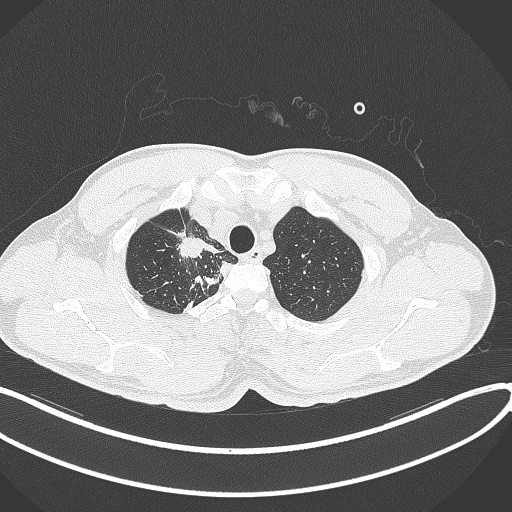
Chest CT, one axial slice; position 329 of 391 along the scan axis; 120 kVp; lung window (W 1500 / L -600 HU); 512 × 512 image matrix, field of view 400 × 400 mm. Male patient, age 48 years. From the clinical record (not read from this slice): clinical TNM (as recorded): T1c N1 M1.
Annotated regions visible in this slice (rectangle marked by the reading radiologist):
- lung tumour (recorded histology: adenocarcinoma): box from (x=176, y=235) to (x=208, y=262) px